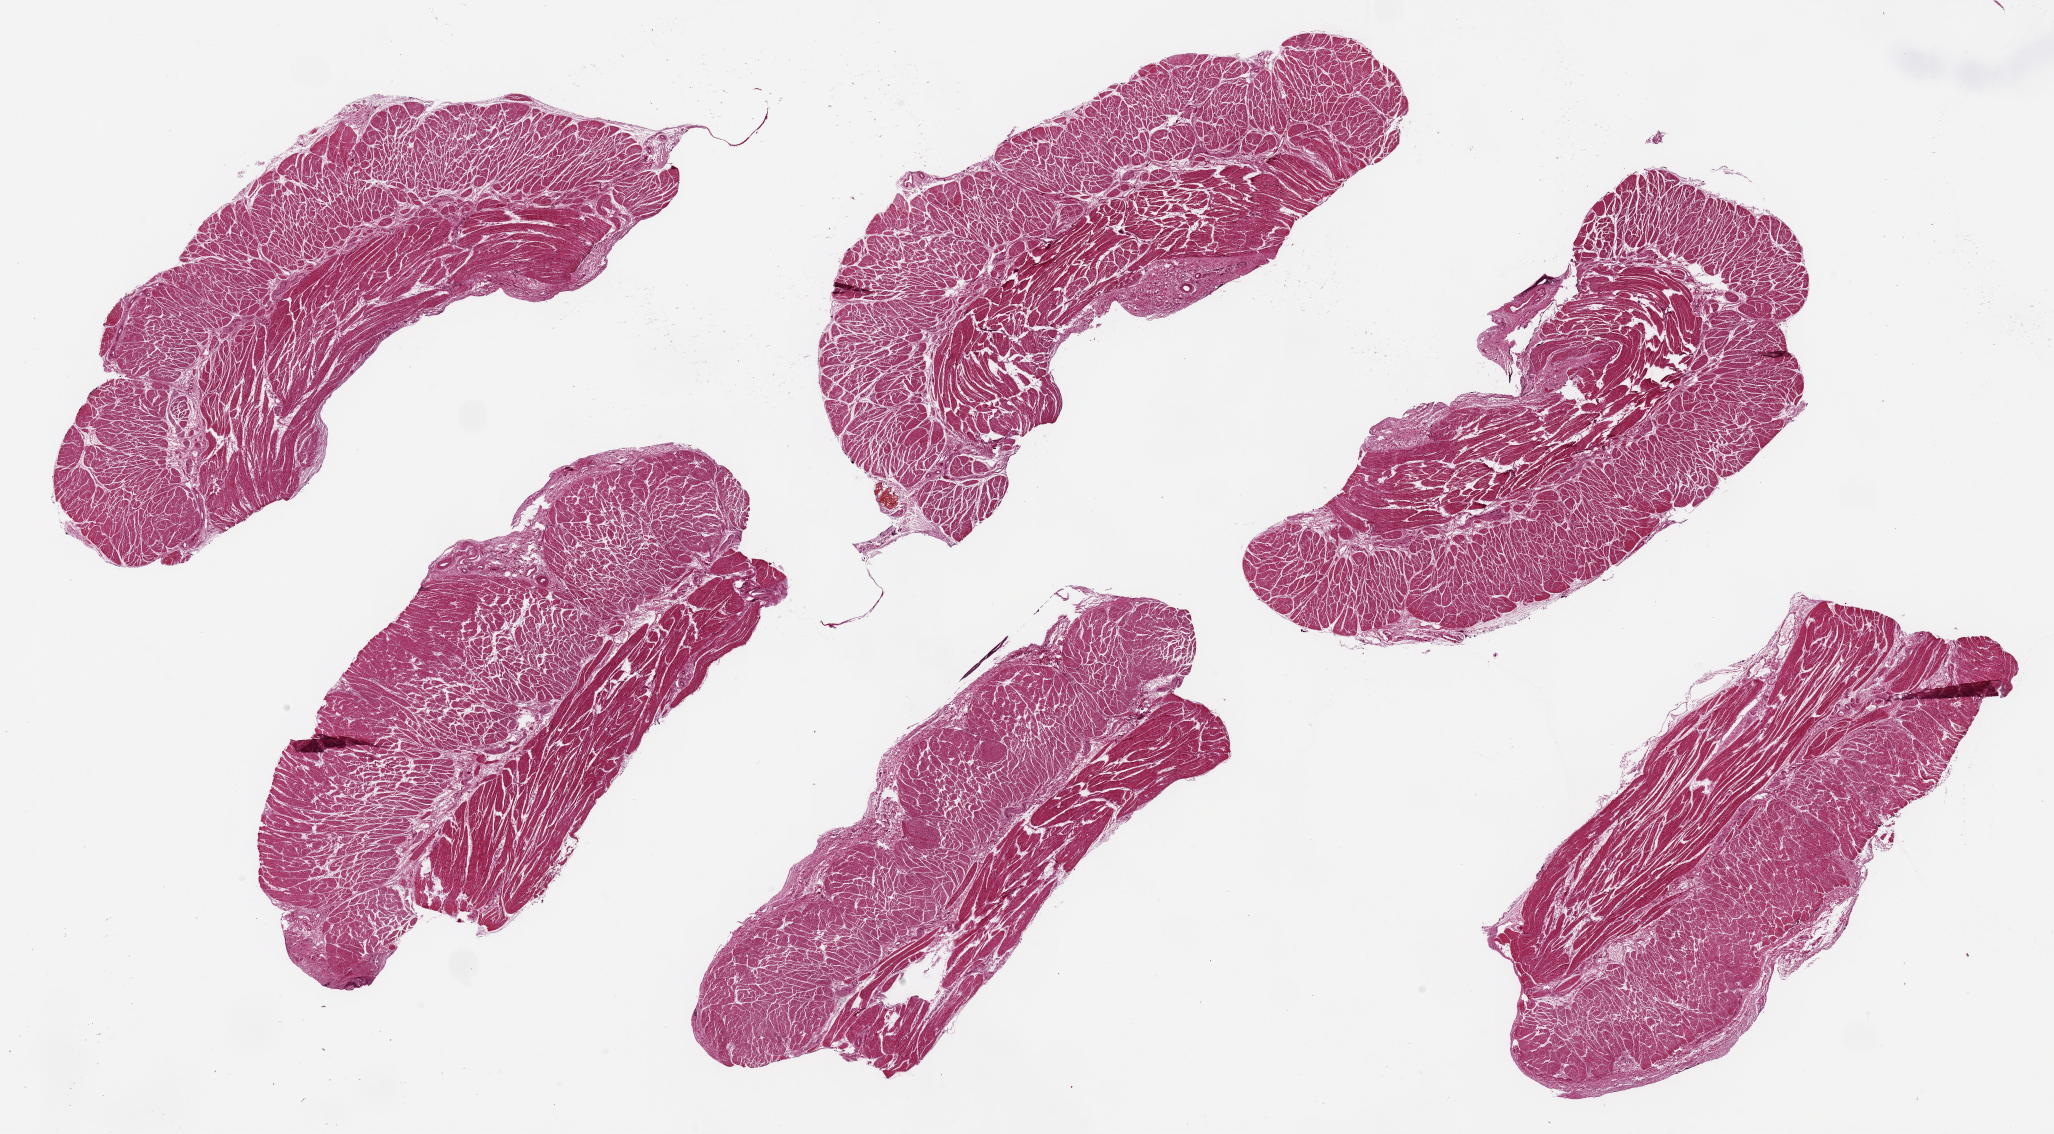
Whole-slide image, H&E stain, brightfield, shown as a low-resolution overview of the whole scanned area (about 32.5 x 17.9 mm); PAXgene-fixed, paraffin-embedded tissue; sampled site (target tissue): esophageal muscle; donor tissue sample. Male donor.
Reviewer comment on this tissue sample: 6 pieces up to 10x4.4 mm.